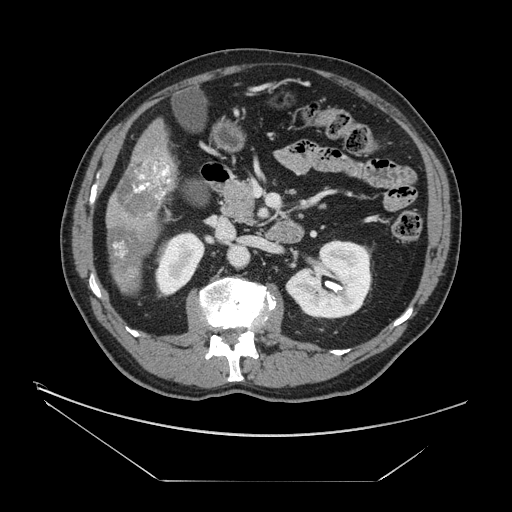
Contrast-enhanced abdominal CT, one axial slice; reconstruction kernel STANDARD; 120 kVp; intravenous contrast given; soft-tissue window (W 400 / L 40 HU); 512 × 512 image matrix, field of view 440 × 440 mm. Male patient, age 65 years. From the clinical record (not read from this slice): diagnosis: colorectal cancer liver metastases, imaged before liver resection; multiple liver metastases: yes; largest metastasis: 4.2 cm; chemotherapy before resection: yes.
Outlined on this slice (expert manual segmentation):
- liver: bounding box (x1, y1, x2, y2) in pixels: (107, 122, 177, 294)
- portal vein (with intrahepatic branches): (134, 161, 170, 199)
- liver metastasis: (109, 228, 147, 270)
- liver metastasis: (117, 161, 174, 218)